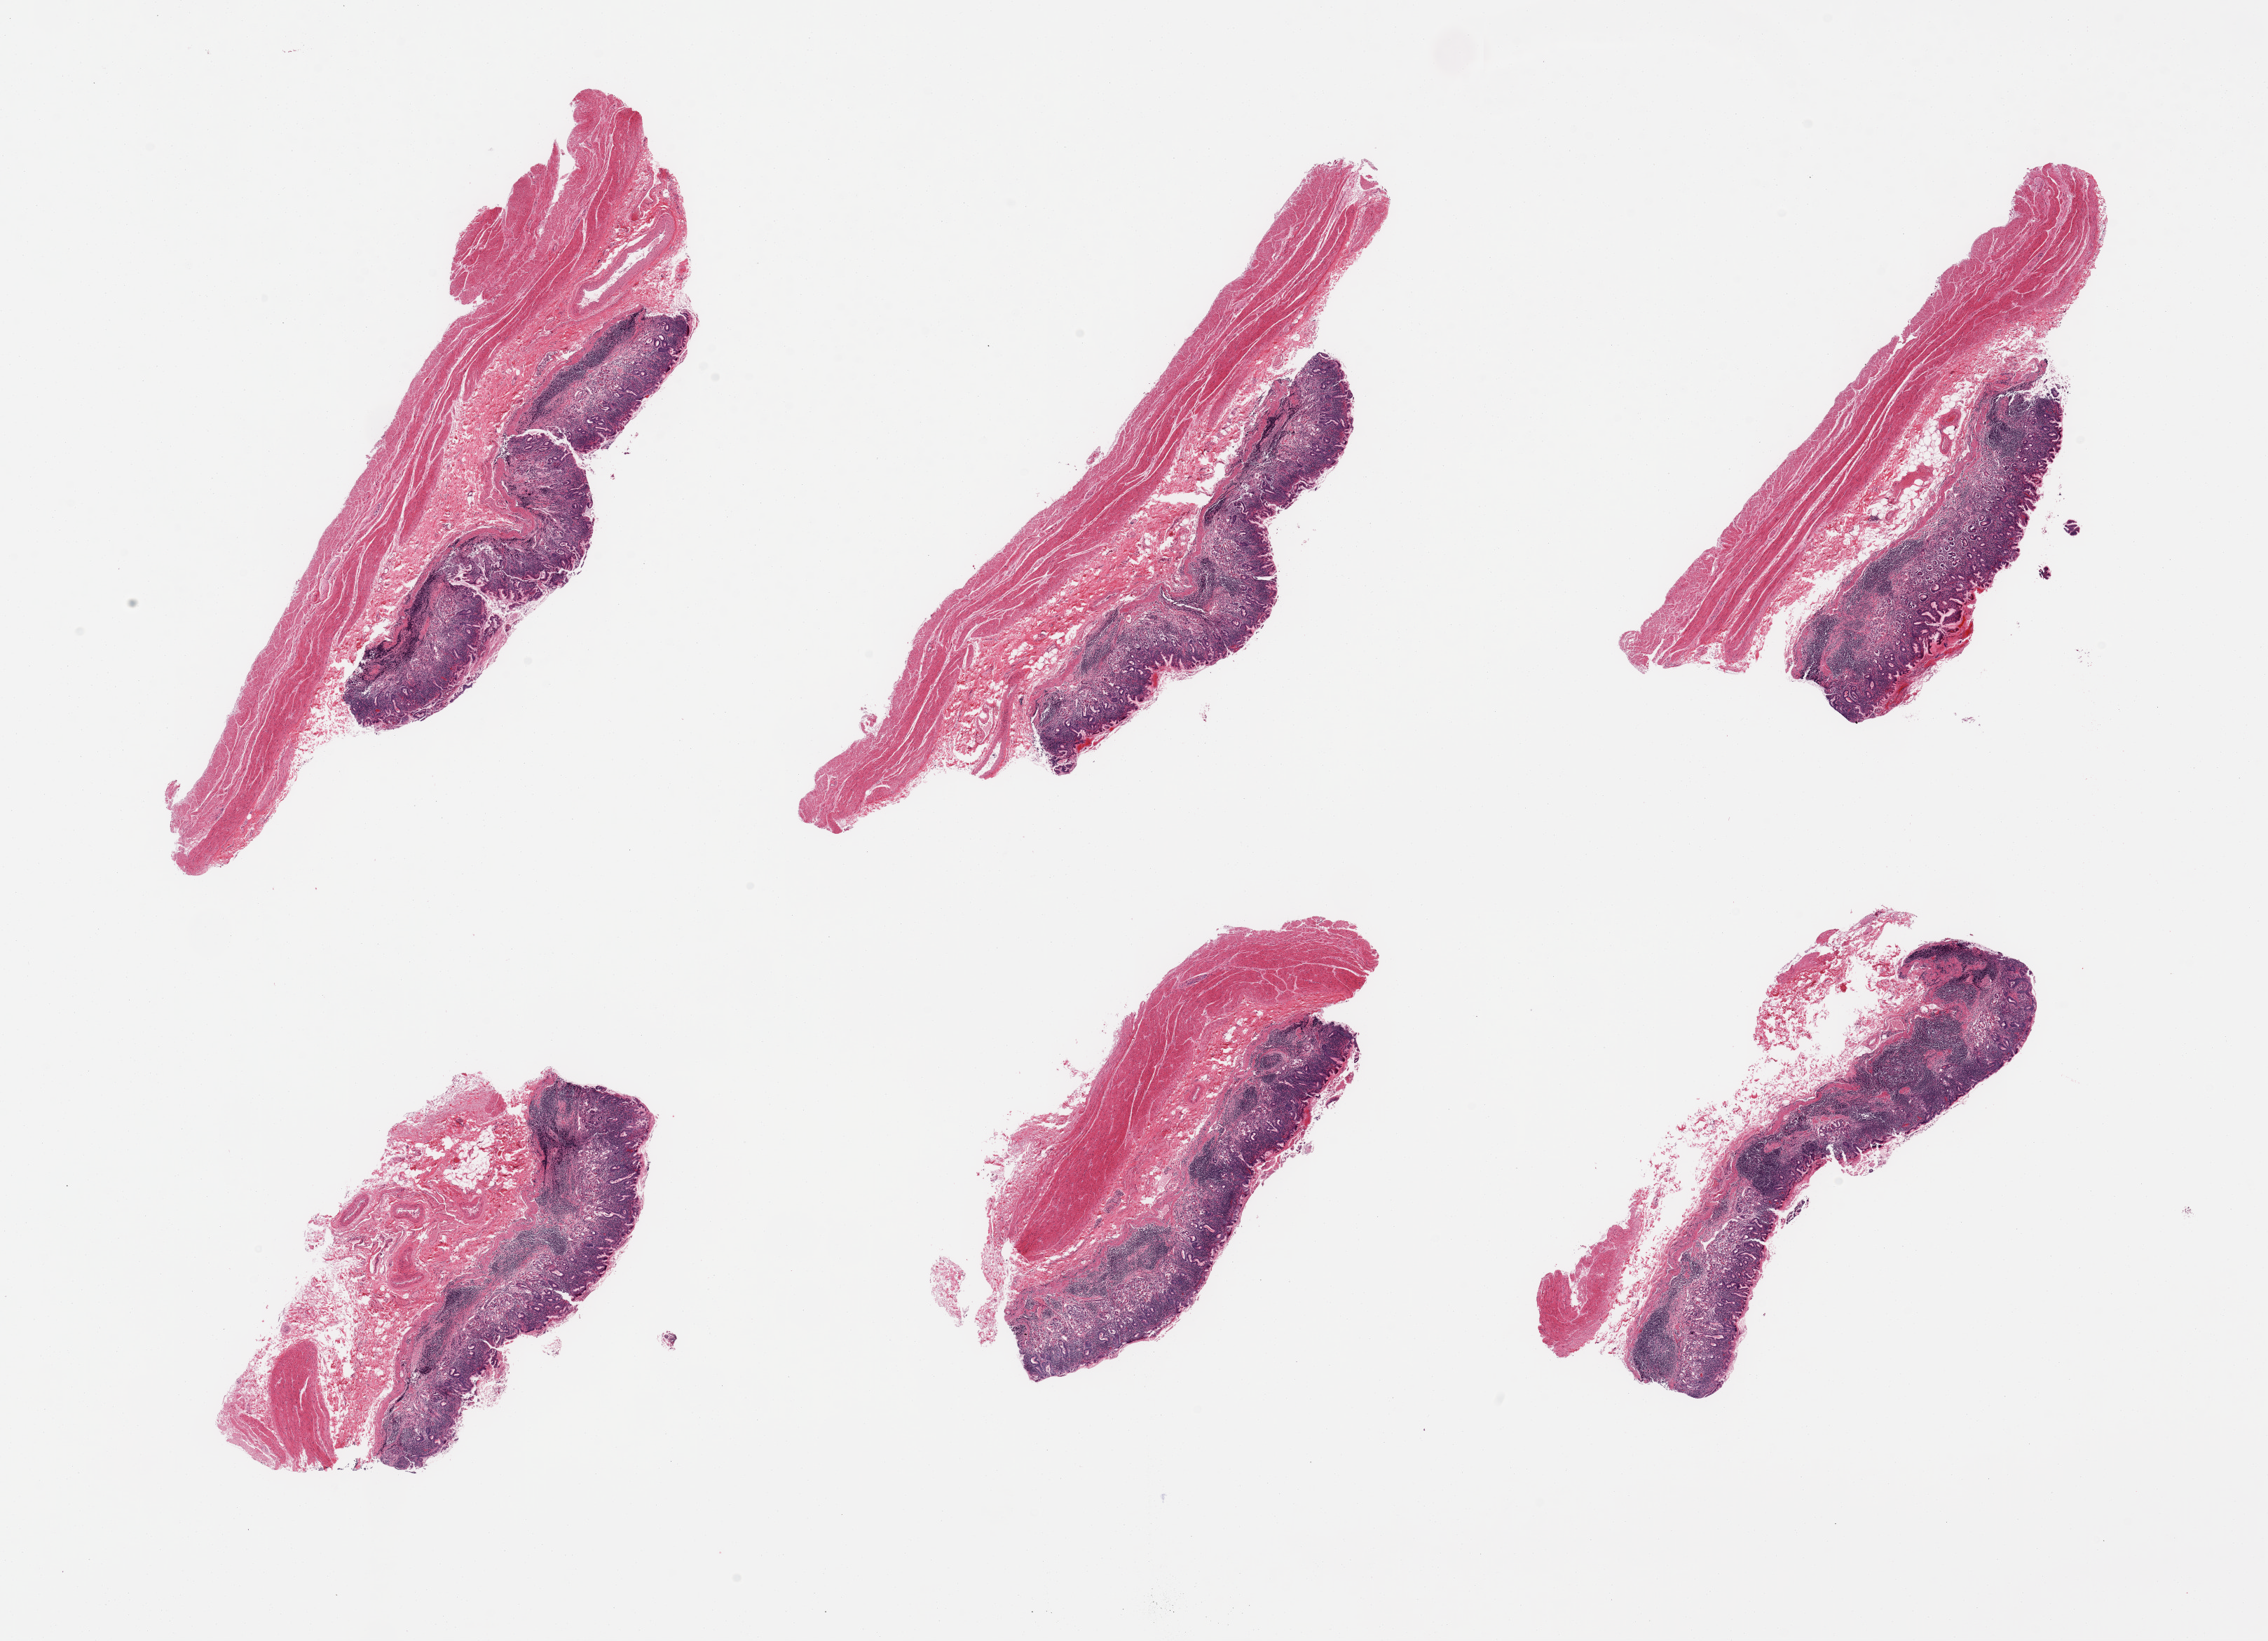
Hematoxylin and eosin (H&E) whole-slide image, brightfield — a low-resolution overview of the entire scanned area, about 25.6 x 18.5 mm, PAXgene-fixed paraffin-embedded (PFPE) section, sampled site (target tissue): stomach, tissue donor sample. Male donor.
Review note (as recorded): 6 pieces, diffuse chronic focally active gastrtitis, pattern suggests H pylori etiology, mucoa up to ~1mm.